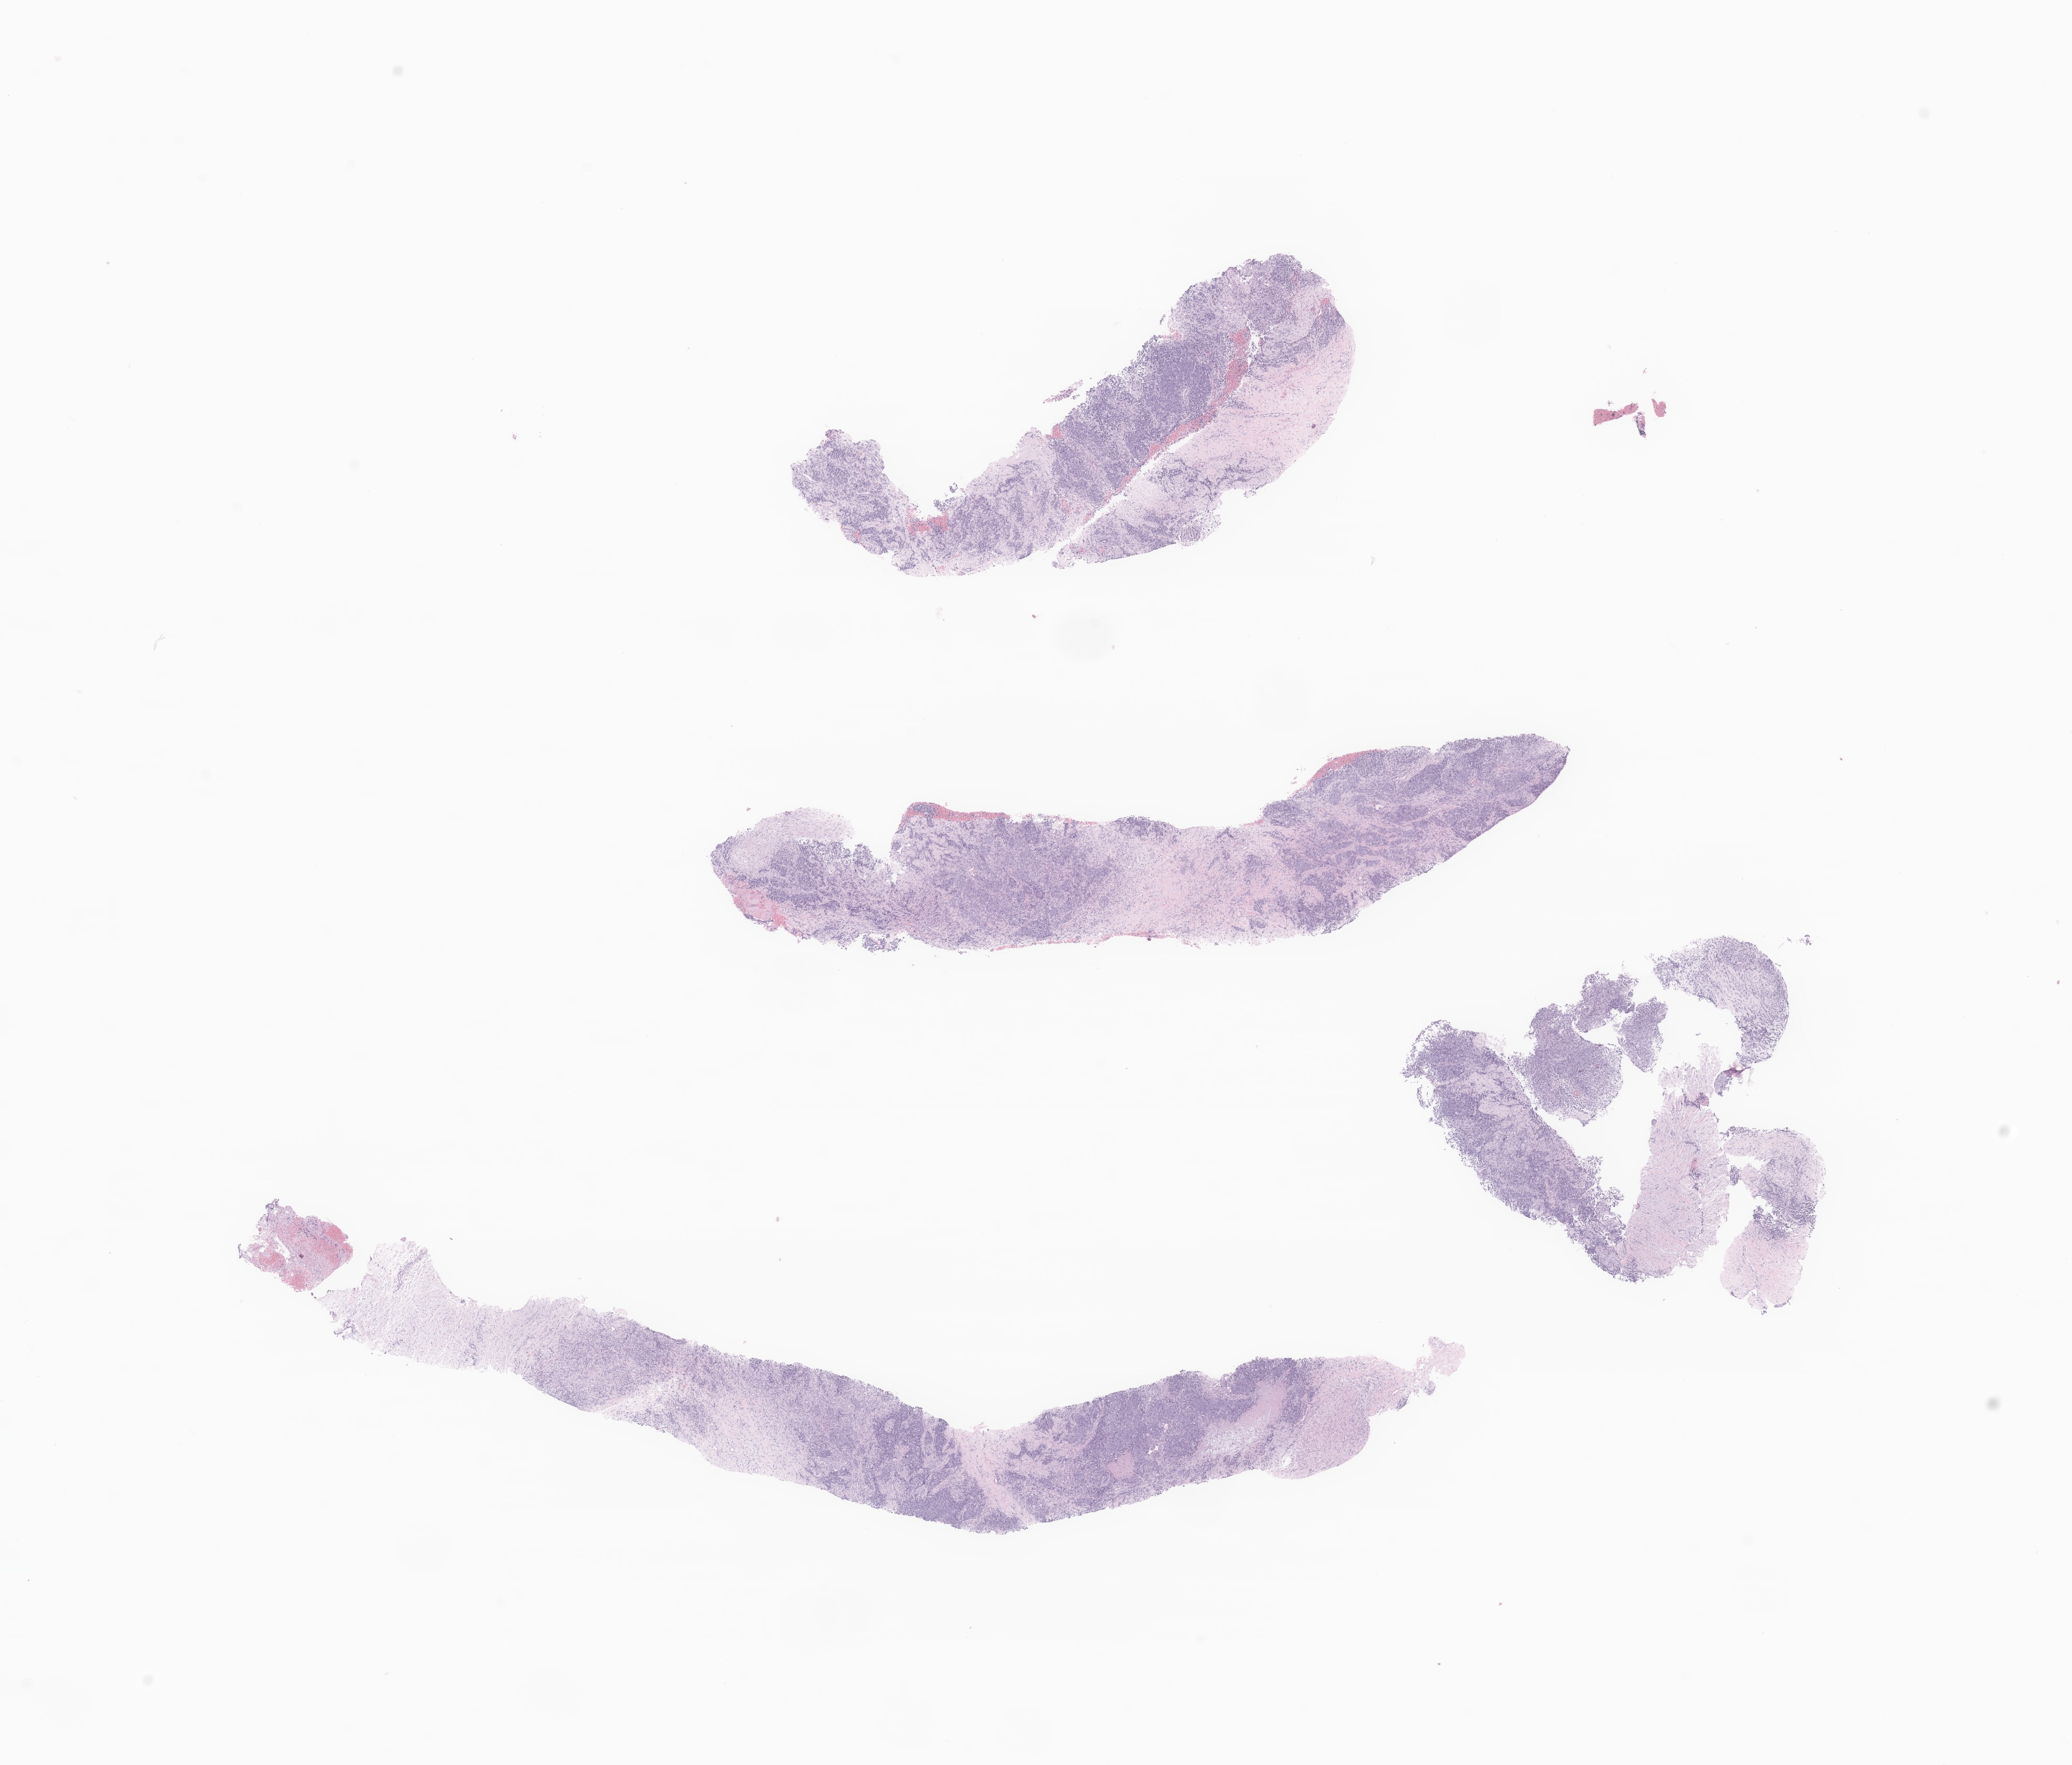
Hematoxylin and eosin (H&E) whole-slide image of tumor tissue from the lower limb — low-resolution overview of the scanned area, about 16.6 x 14.2 mm; FFPE section. Female patient, age 569 days (about 1.6 years).
Recorded diagnosis: Undifferentiated sarcoma.